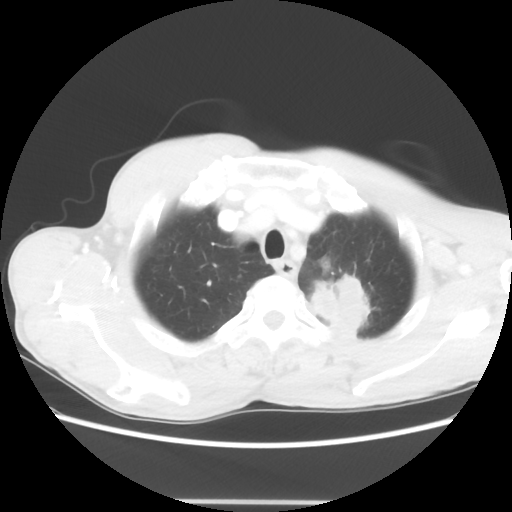
Chest CT, one axial slice. Slice 56 of 62 in the series (ordered by position). Lung window (W 1500 / L -600 HU). 5 mm slice thickness. 512 × 512 image matrix. Male patient, age 61 years. Case-level facts recorded for this patient, not image findings: clinical TNM (as recorded): T3 N1 M1.
Outlined on this slice (rectangle marked by the reading radiologist):
- lung tumour (recorded histology: adenocarcinoma): bounding box (x1, y1, x2, y2) in pixels: (308, 271, 374, 337)